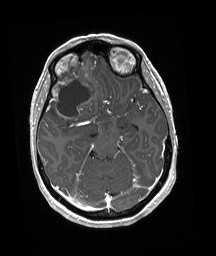
Brain MRI from a brain-tumour surgery series, one axial slice; slice 118 of 192 in the series (ordered by position); T1-weighted post-contrast; 1 mm slice thickness; 216 × 256 image matrix, field of view 211 × 250 mm. Case-level facts recorded for this patient, not image findings: histopathology: Oligodendroglioma; WHO grade: 3; IDH mutation: yes; tumour location: Right Frontal.
Structures marked on this image (manually delineated by an expert):
- tumour: bounding box <49,63,97,122> (left, top, right, bottom; pixels)